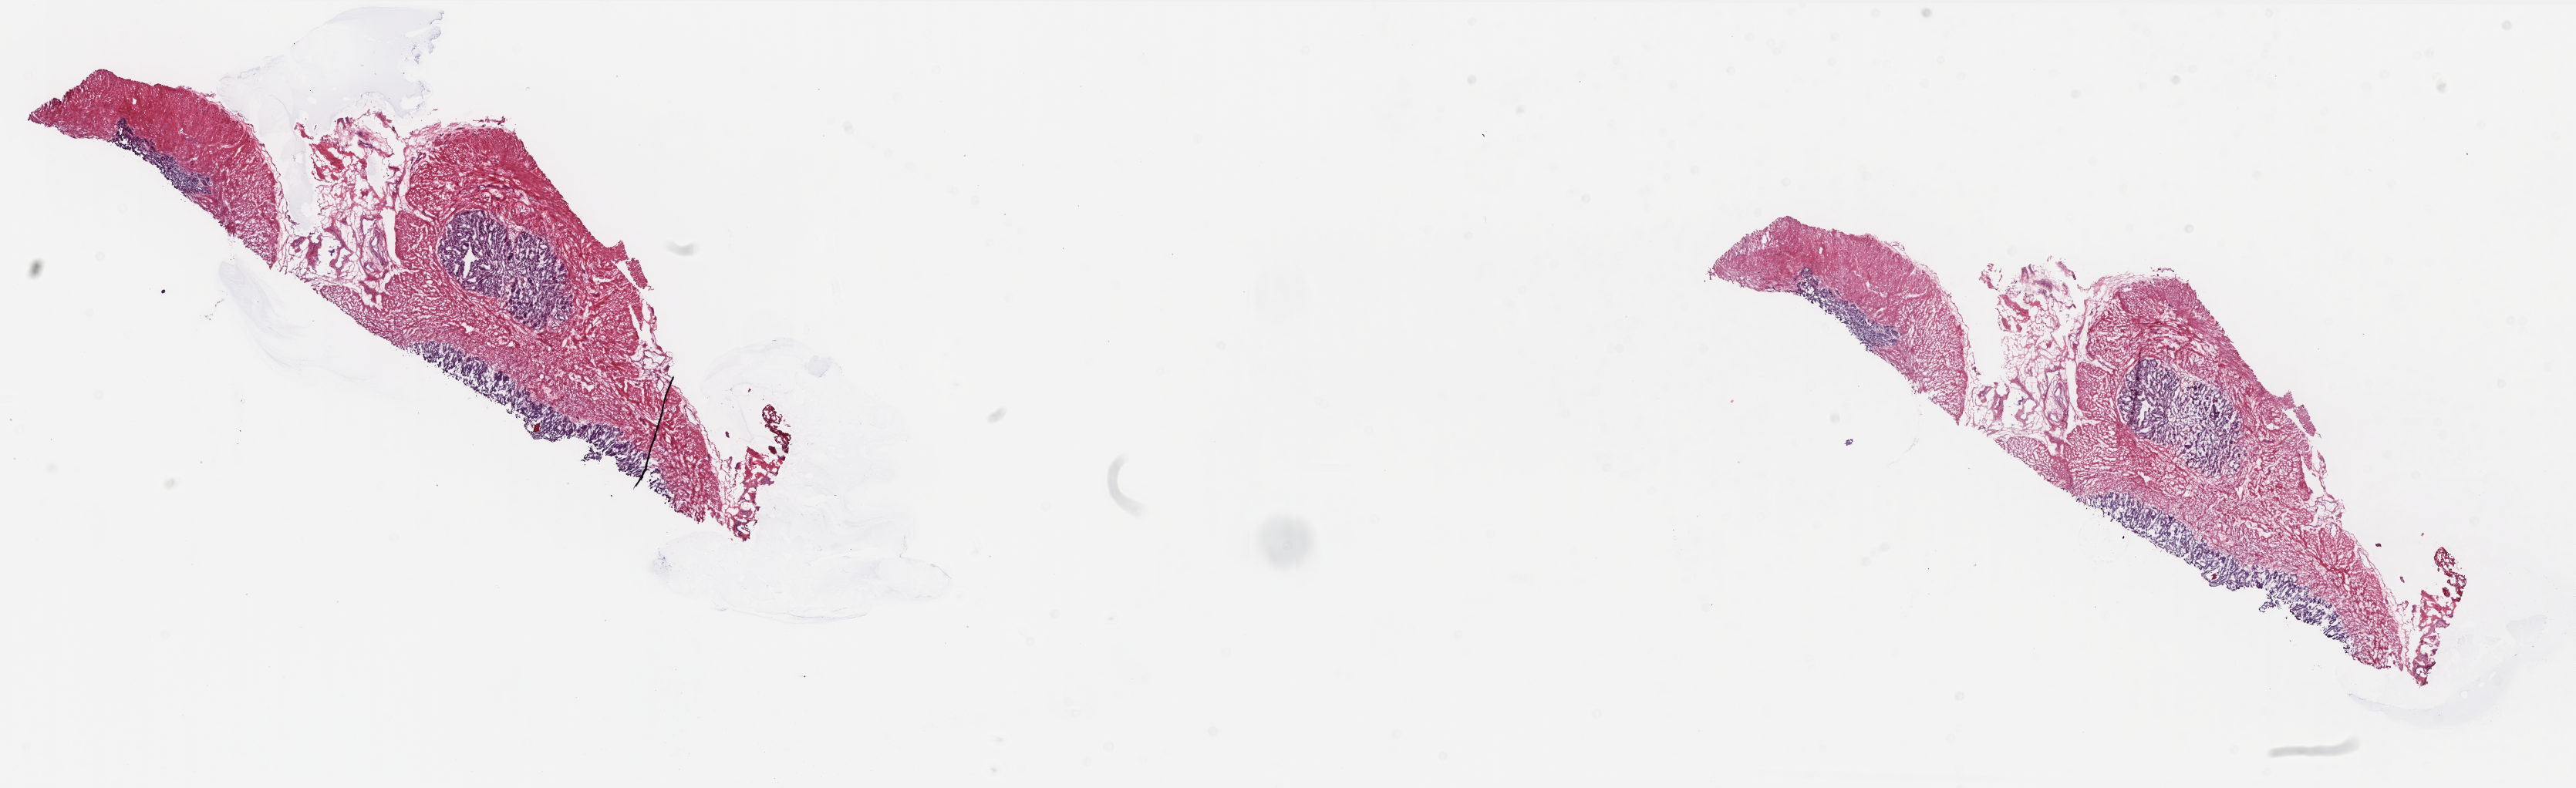
Hematoxylin and eosin (H&E) stained whole-slide image — a low-resolution overview of the entire scanned area, about 26.9 x 8.2 mm. Frozen section from the top of the tissue portion. Prostate, solid tissue normal (non-tumour tissue) sample. Patient: male, age at initial diagnosis 56 years. Pathologist review of this section (percent, as recorded): tumour cells 0%, tumour nuclei 0%, normal cells 100%, stromal cells 0%, necrosis 0%. Infiltration values recorded for this section: lymphocyte infiltration 0%, monocyte infiltration 0%, neutrophil infiltration 0%.
- this section: solid tissue normal (non-tumour) sample from the same patient
- patient diagnosis: Adenocarcinoma, NOS (prostate gland)